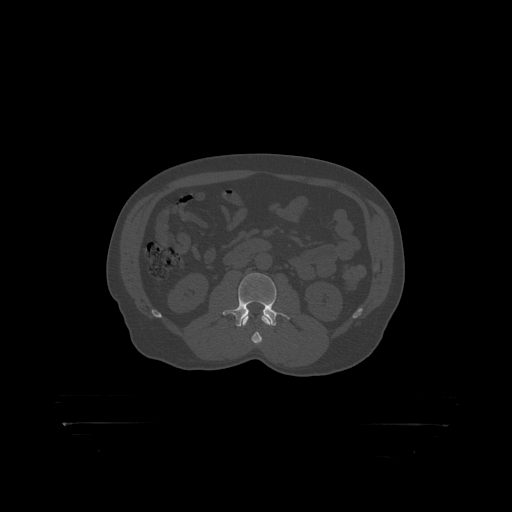
CT including the spine, one axial slice; position 276 of 399 along the scan axis; reconstruction kernel STANDARD; 120 kVp; bone window (W 1800 / L 400 HU); 512 × 512 image matrix, field of view 650 × 650 mm. Patient: male, 46 years. Case-level facts recorded for this patient, not image findings: primary cancer: skin.
Outlined on this slice (semi-automatically segmented with operator editing):
- L2 vertebra: box from (x=244, y=315) to (x=265, y=319) px
- L3 vertebra: (x=227, y=273)–(x=281, y=319)